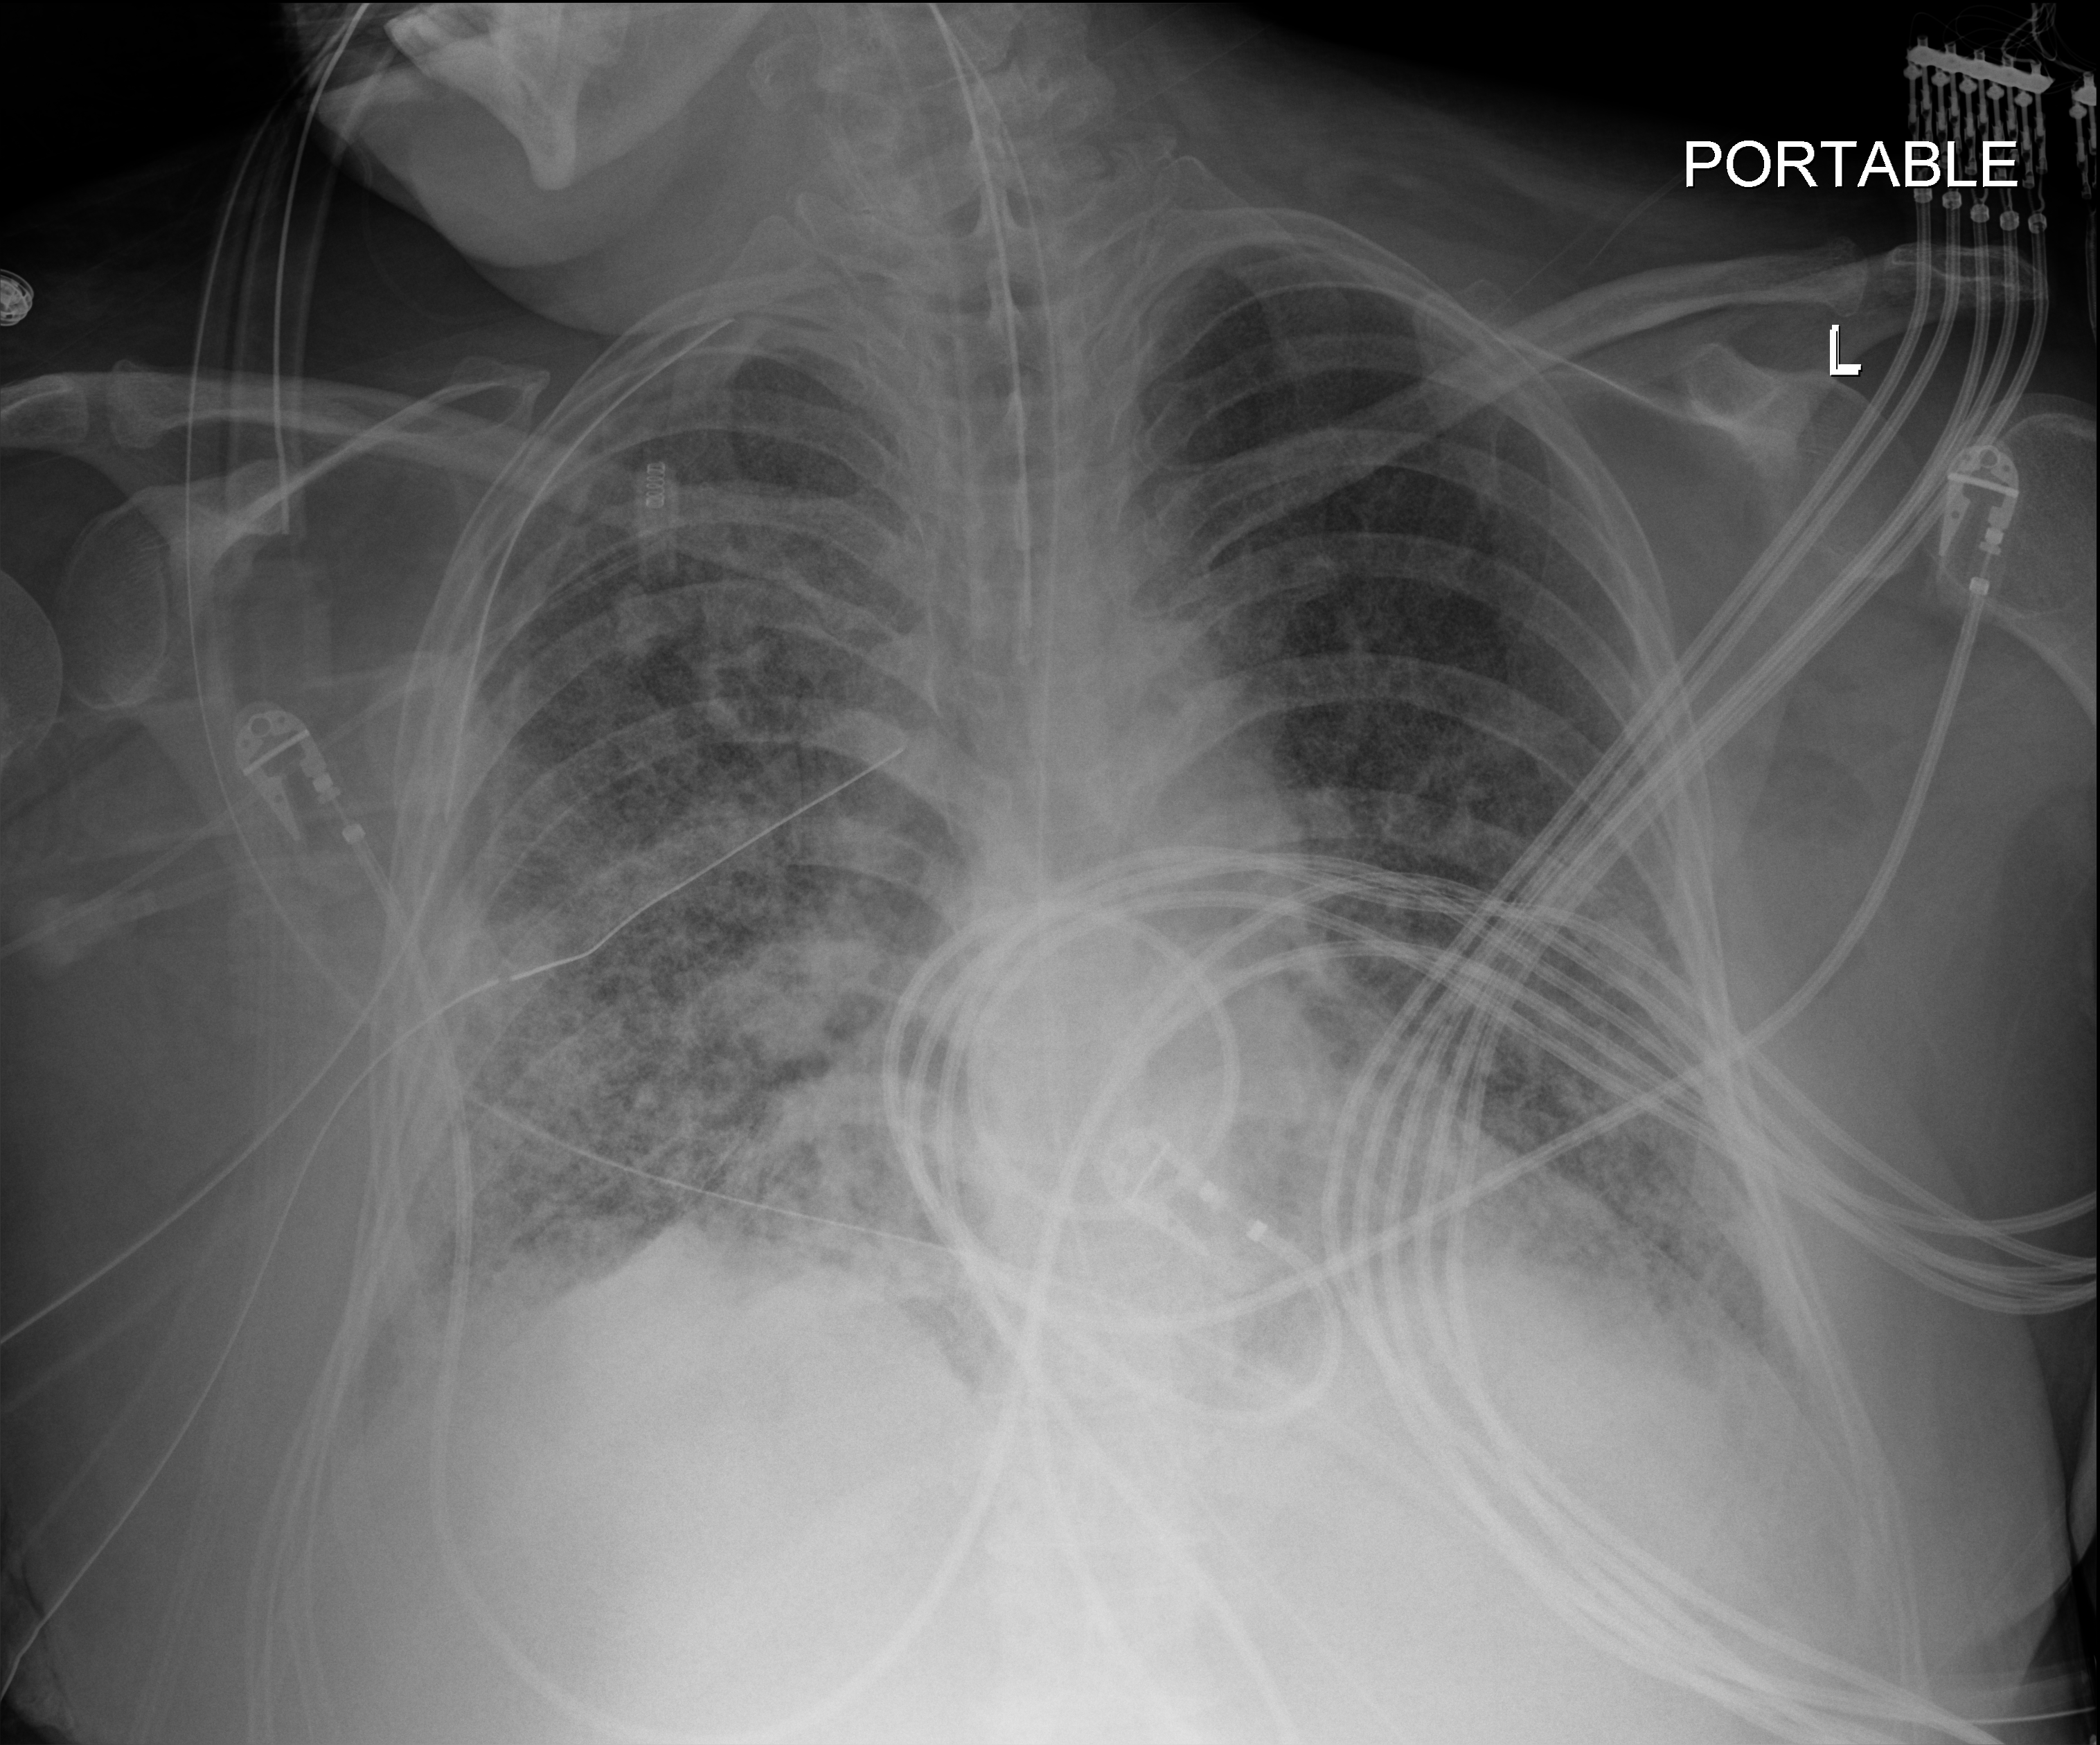
Chest X-ray (portable); anteroposterior (AP) projection. Adult patient hospitalised with COVID-19, age 18–59 years.
From the hospital-stay record, not from the radiograph (when in the stay this image was taken is not recorded):
- admitted to intensive care during this hospital stay: yes
- other chronic lung disease (admission record): no
- mechanically ventilated during this hospital stay: yes